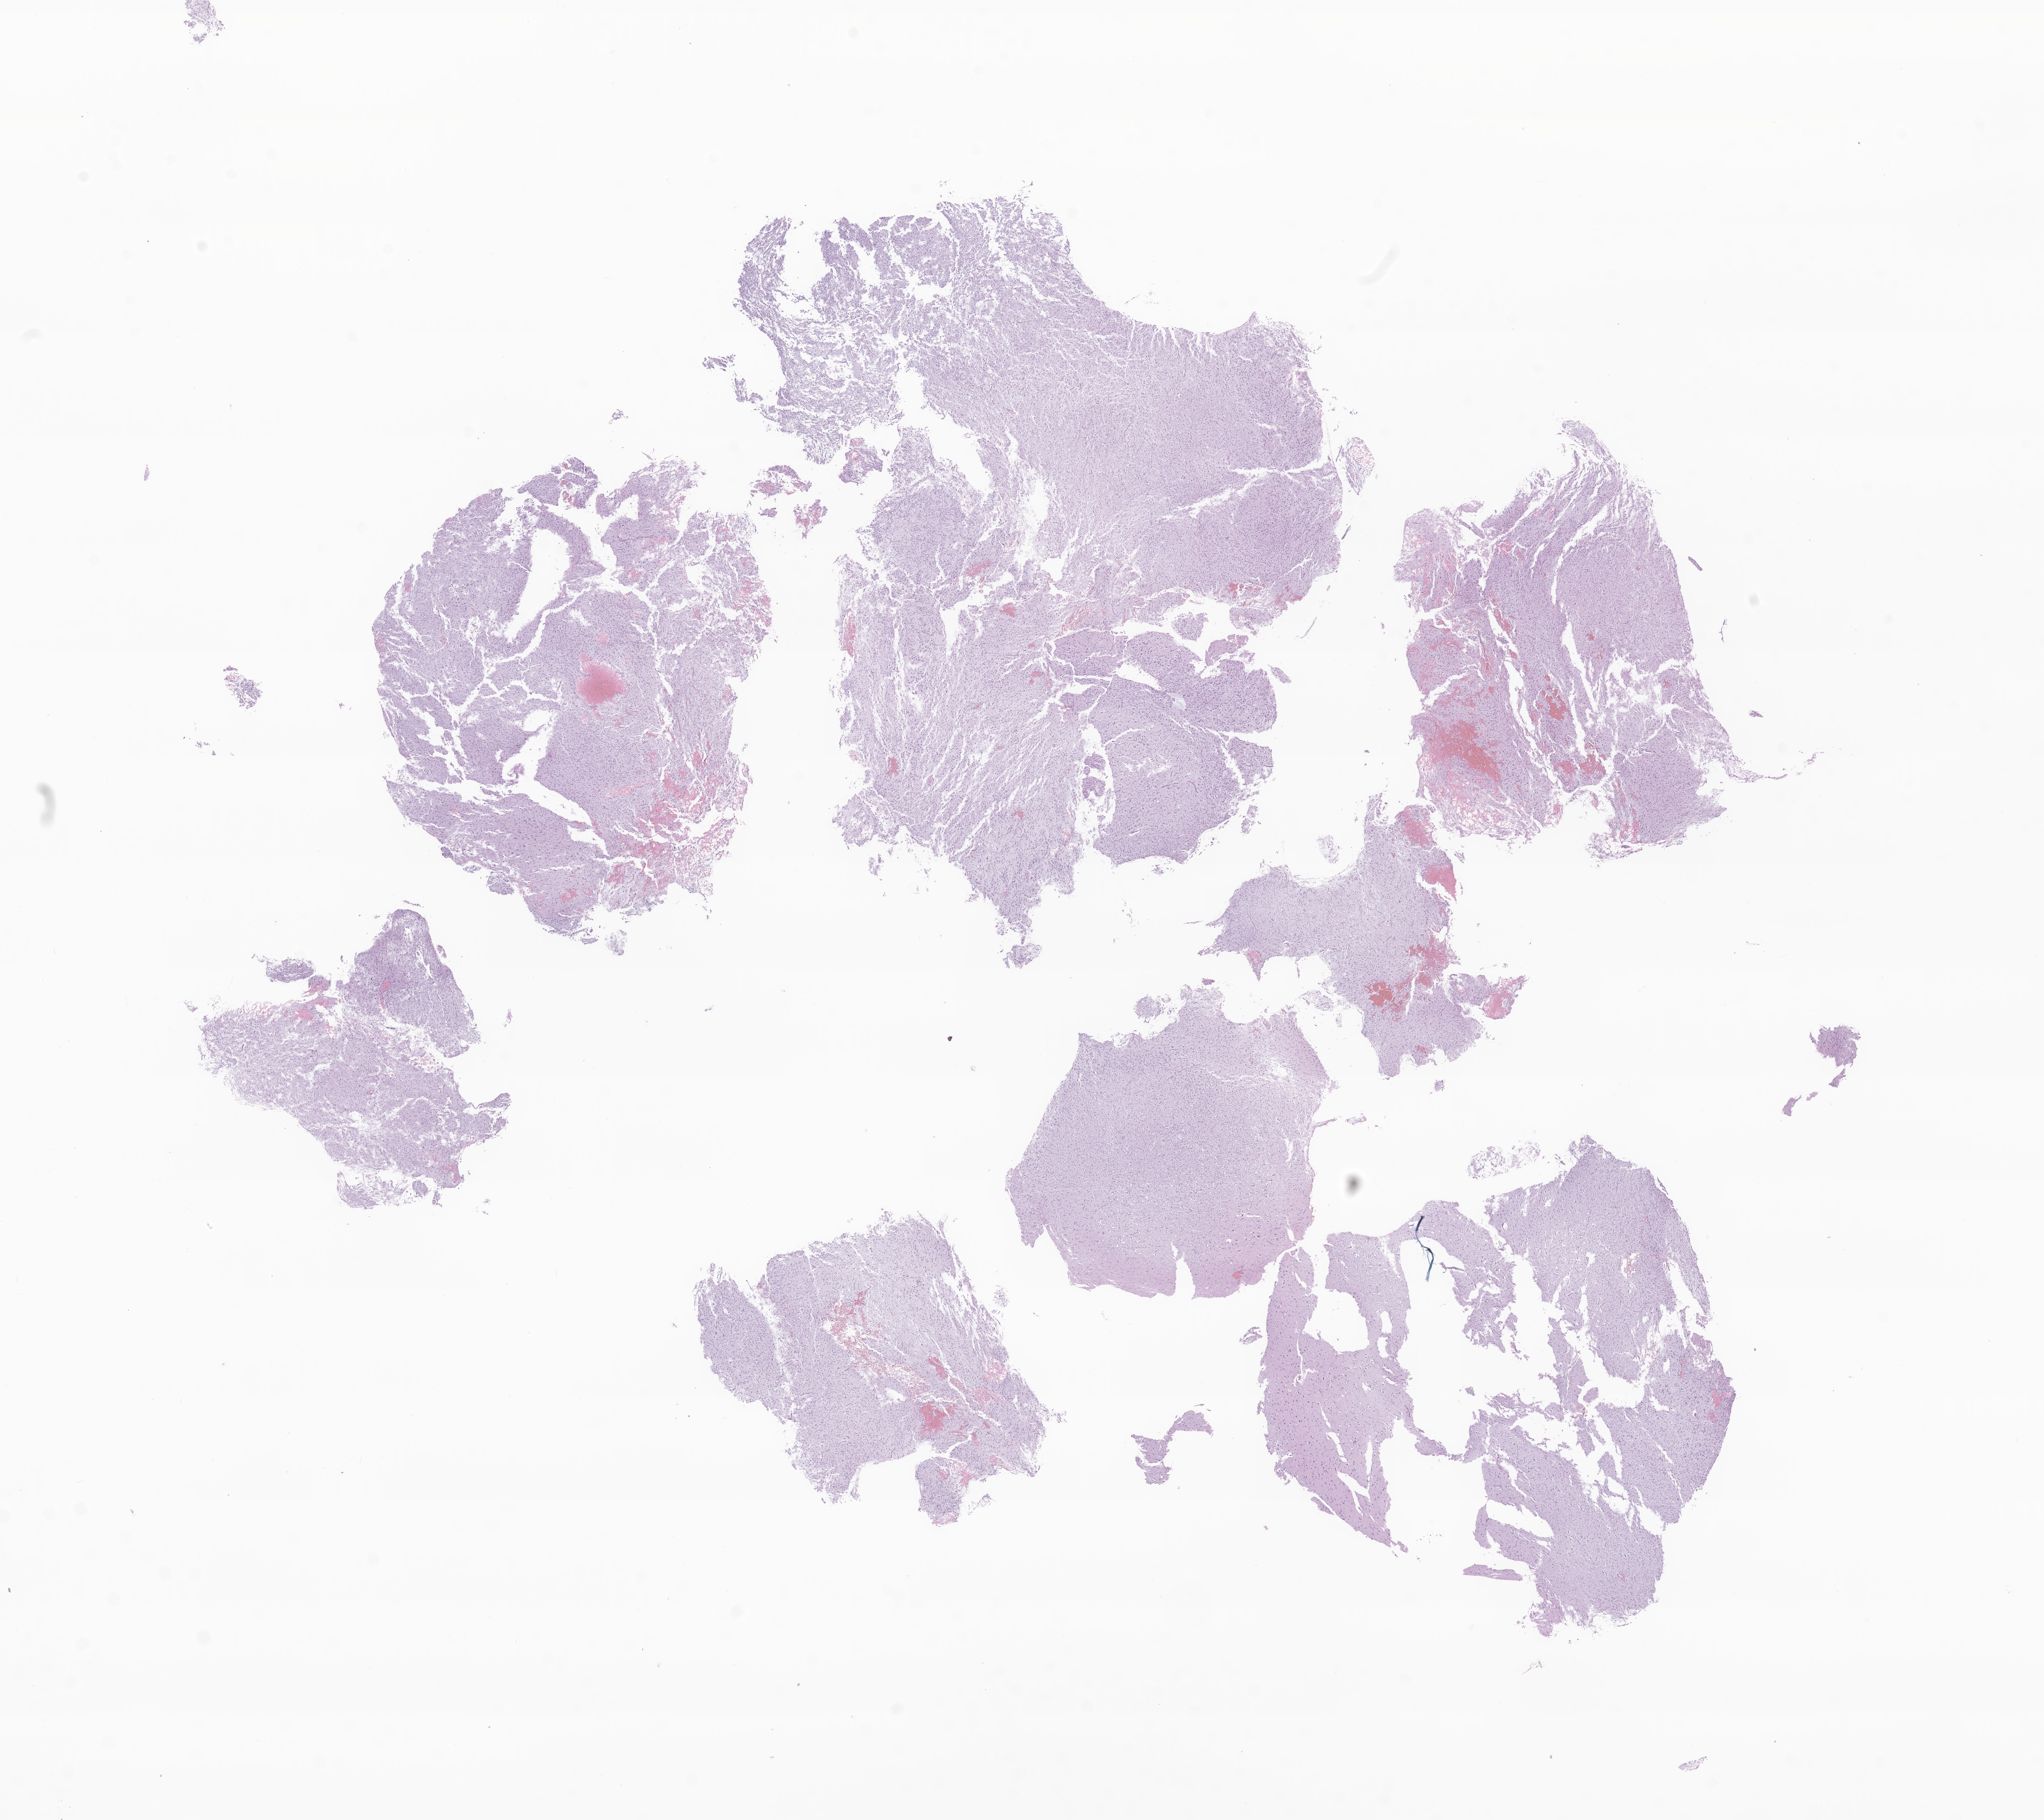
Whole-slide image, hematoxylin and eosin (H&E) stain of tumor tissue from the brain — low-resolution overview of the scanned area, about 20.5 x 18.3 mm. Formalin-fixed paraffin-embedded section. Patient female; age 38 months (3 years 2 months).
Diagnosis: Ganglioglioma, NOS.